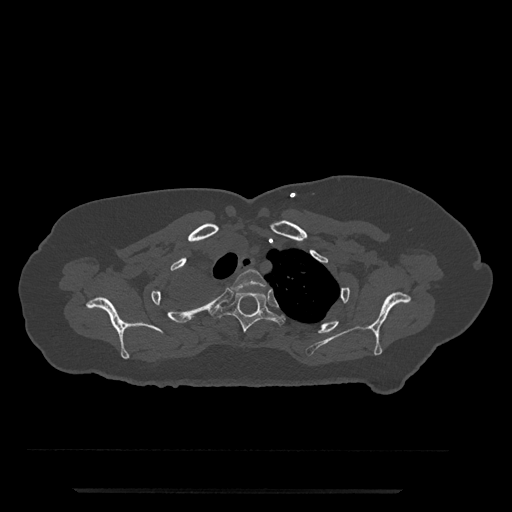
CT including the spine, one axial slice; position 641 of 797 along the scan axis; bone window (W 1800 / L 400 HU); 0.5 mm slice thickness; 512 × 512 image matrix, field of view 440 × 440 mm. Female patient, age 51 years. Case-level facts recorded for this patient, not image findings: primary cancer: neuro; vertebrae with lytic lesions (as recorded): T8.
Outlined on this slice (semi-automatic segmentation, software-assisted and operator-edited):
- T2 vertebra: bounding box [x1, y1, x2, y2] px = [232, 269, 267, 291]
- T3 vertebra: [213, 291, 285, 333]